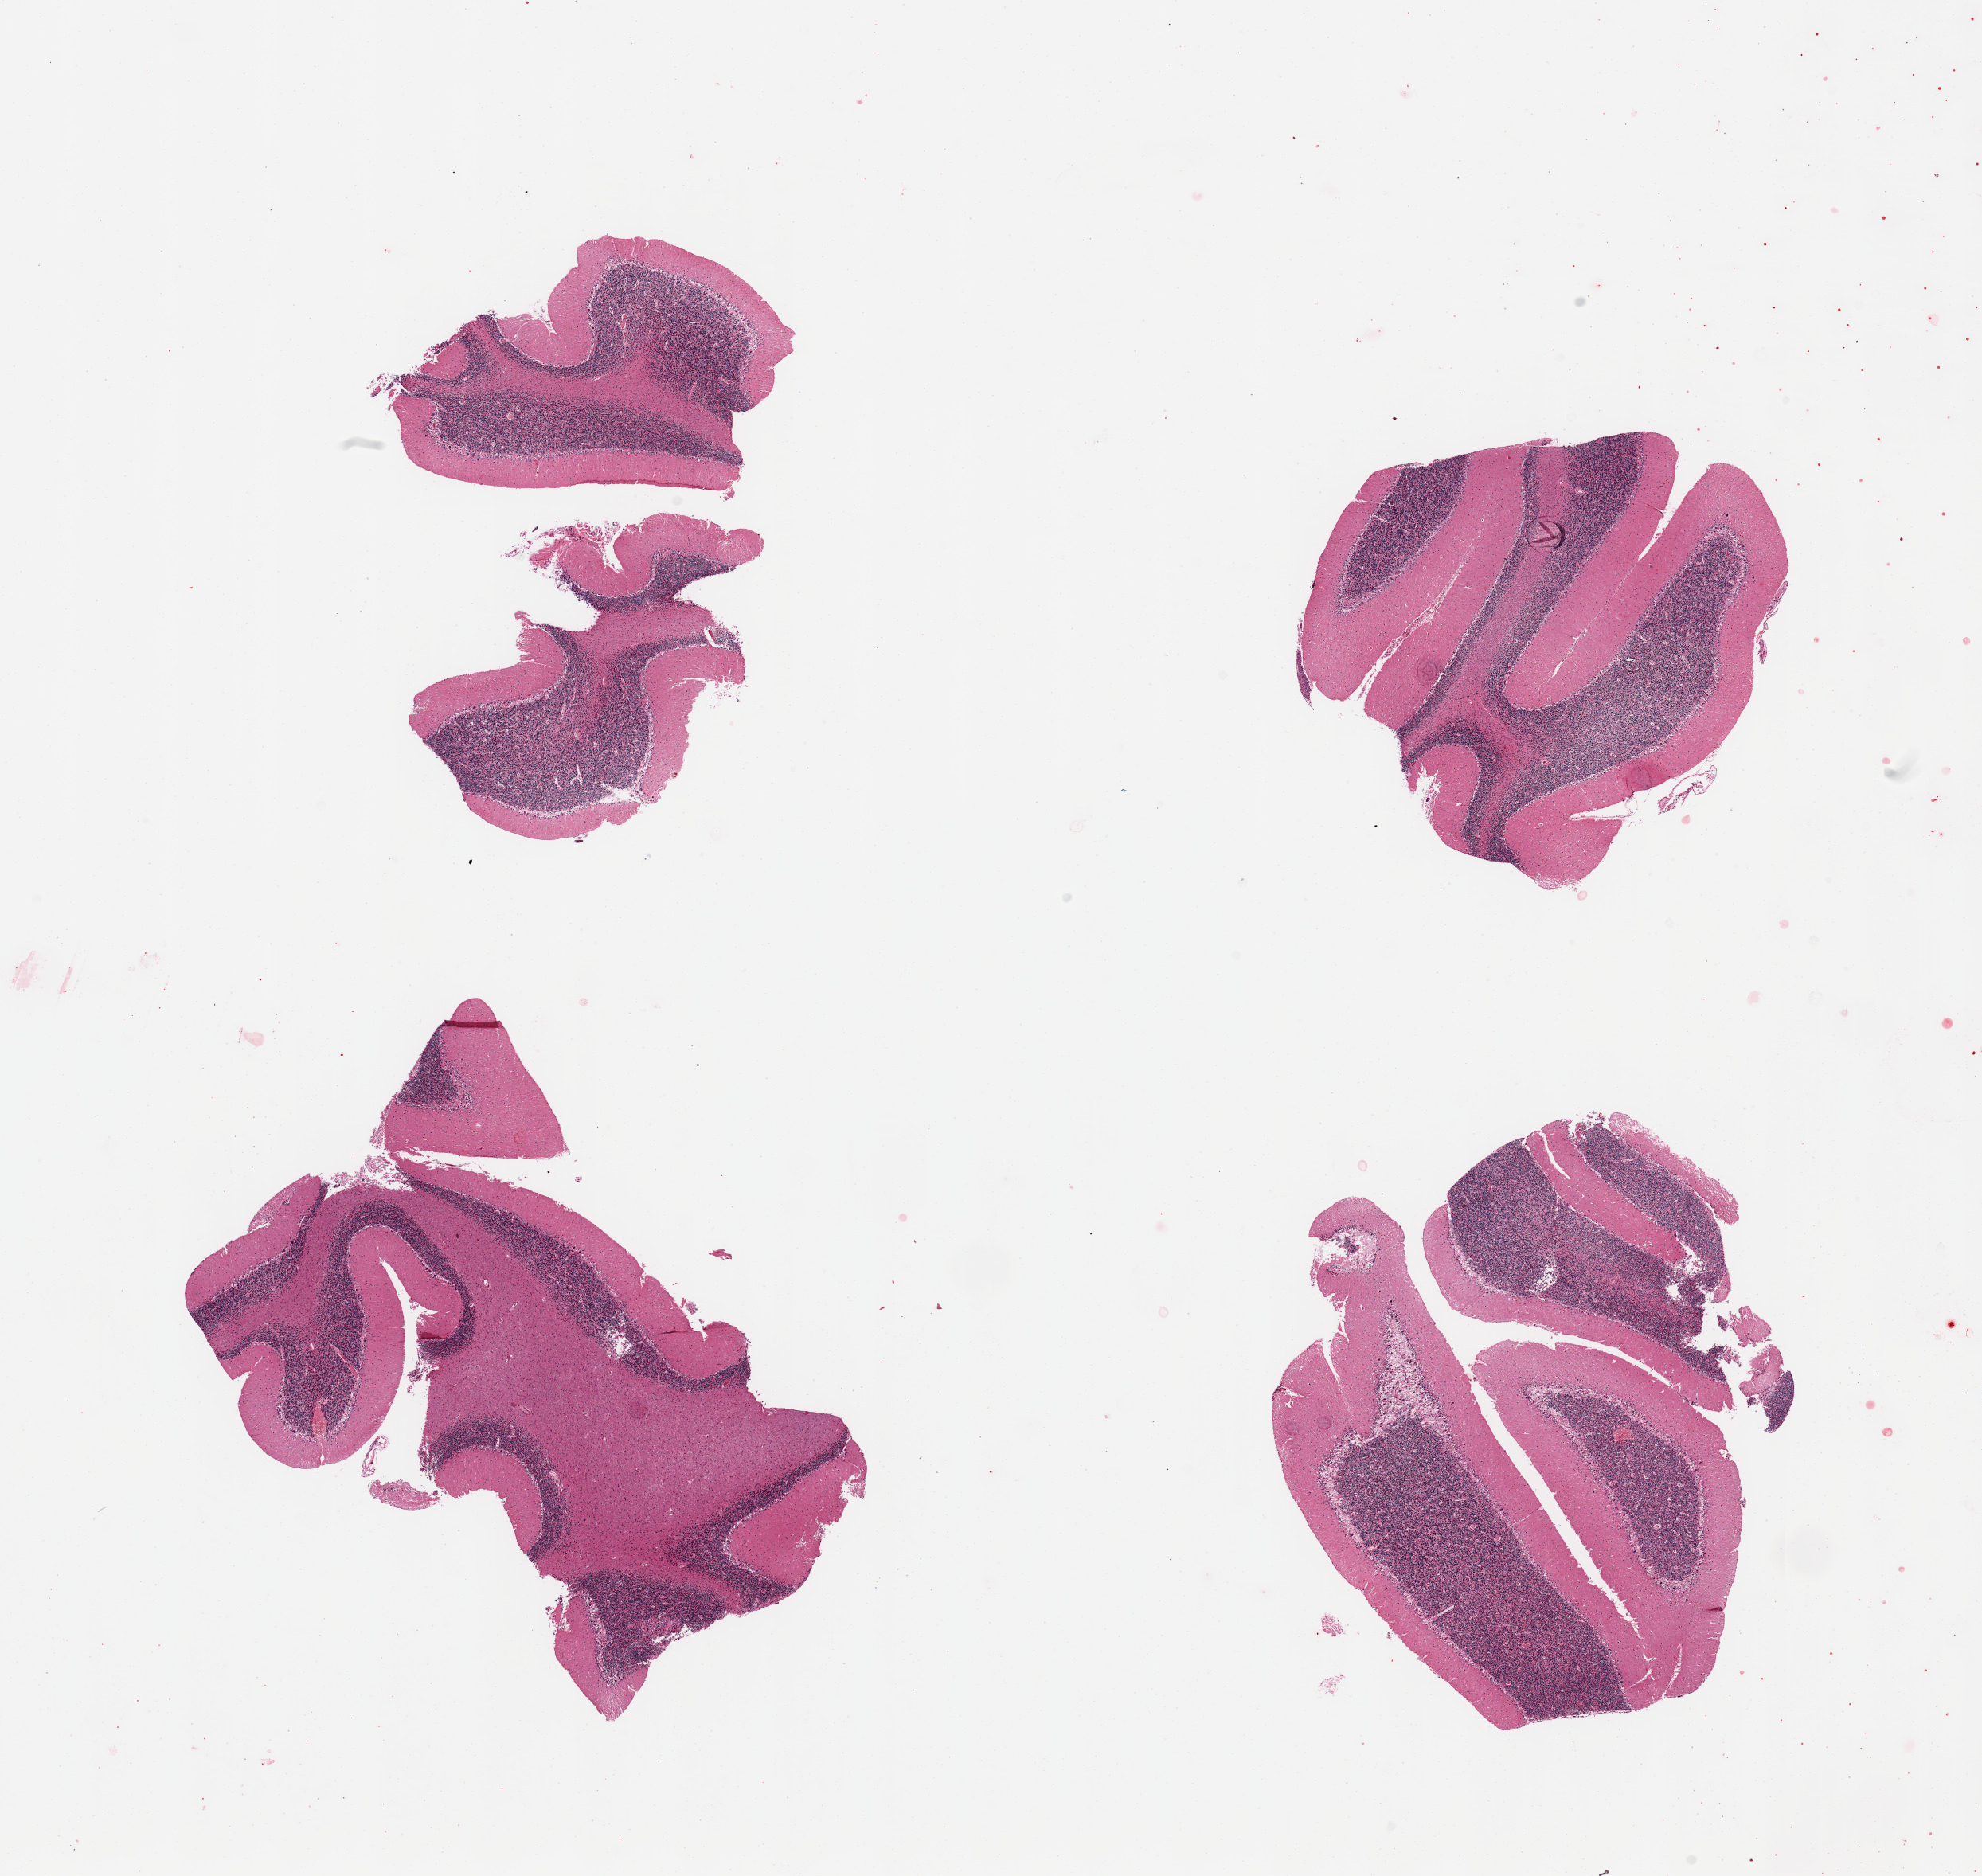
Haematoxylin and eosin whole-slide image, low-resolution overview of the scanned area, about 19.7 x 18.6 mm (from a 20x scan). PAXgene-fixed paraffin-embedded (PFPE) section. Section of cerebellum (target tissue). Tissue donor sample. Donor sex: female.
* reviewer comment on this tissue sample: 4 pieces, no abnormalities